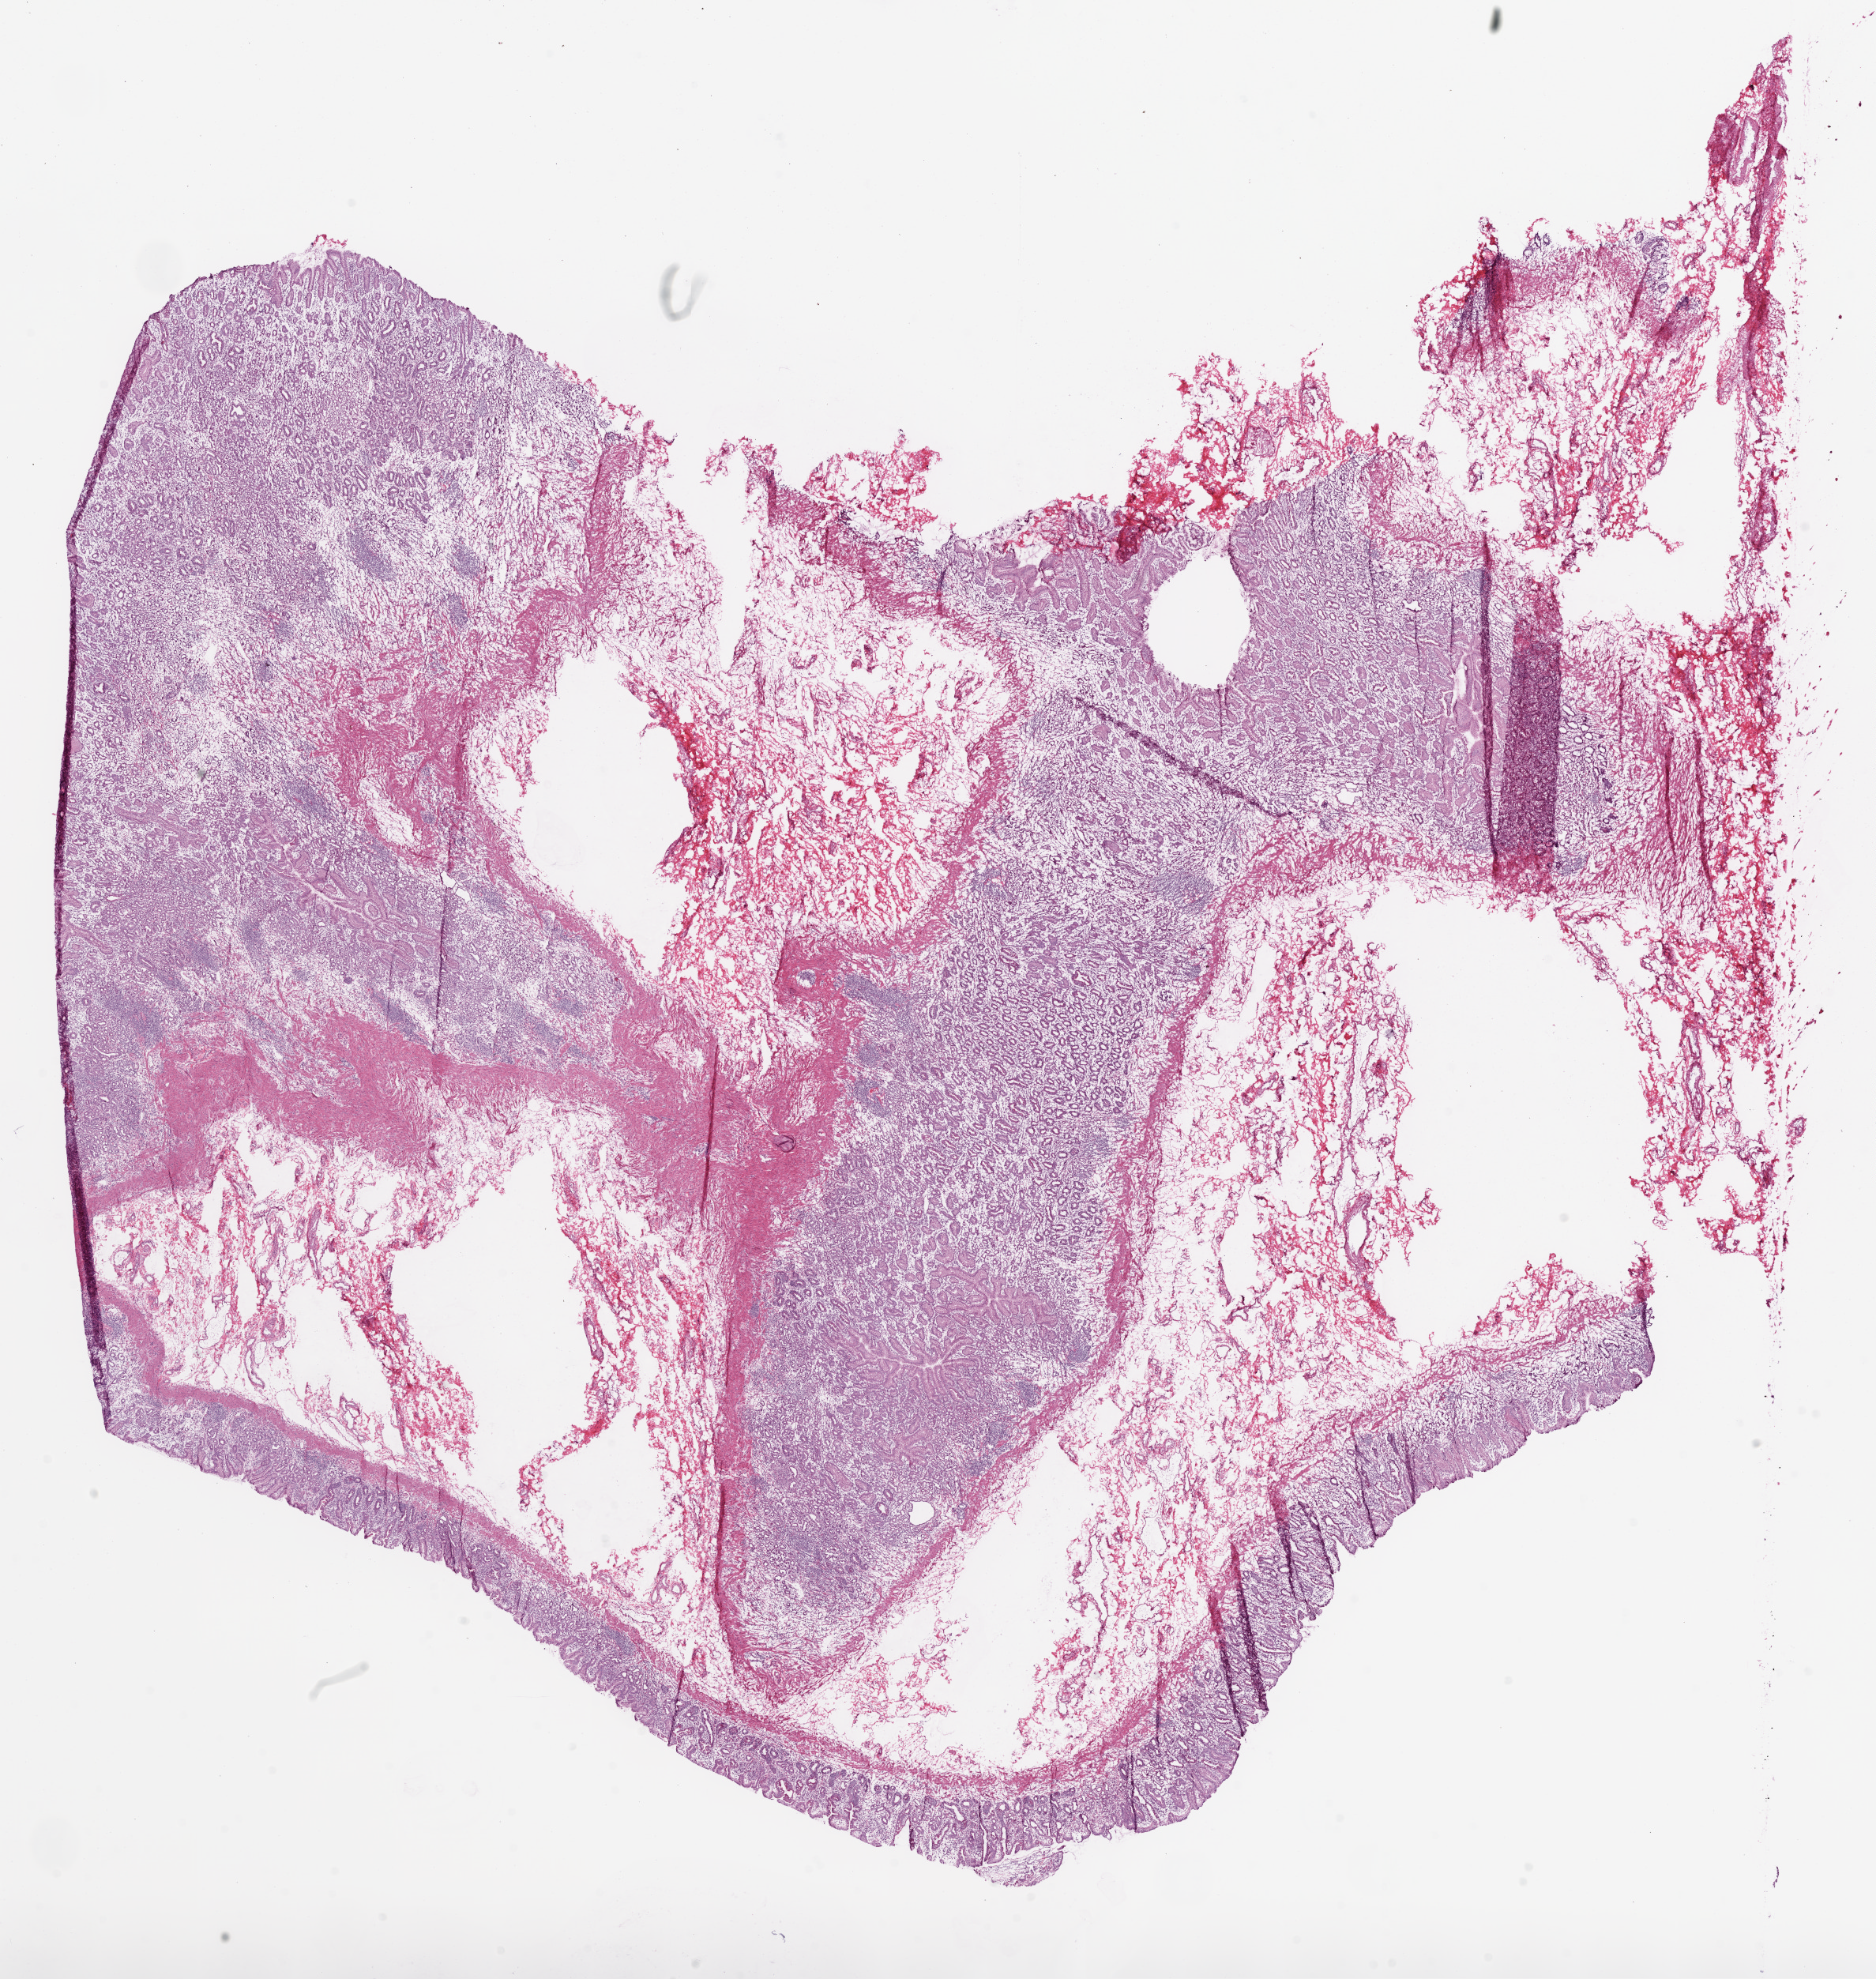
H&E-stained whole-slide image, low-resolution overview of the scanned area, about 19.1 x 20.1 mm (slide scanned at 20x), frozen section from the top of the tissue portion, sample: solid tissue normal (non-tumour tissue), stomach. Female, age 73 years at initial diagnosis.
This section: solid tissue normal (non-tumour) sample from the same patient. Patient diagnosis: Adenocarcinoma, NOS (body of stomach).